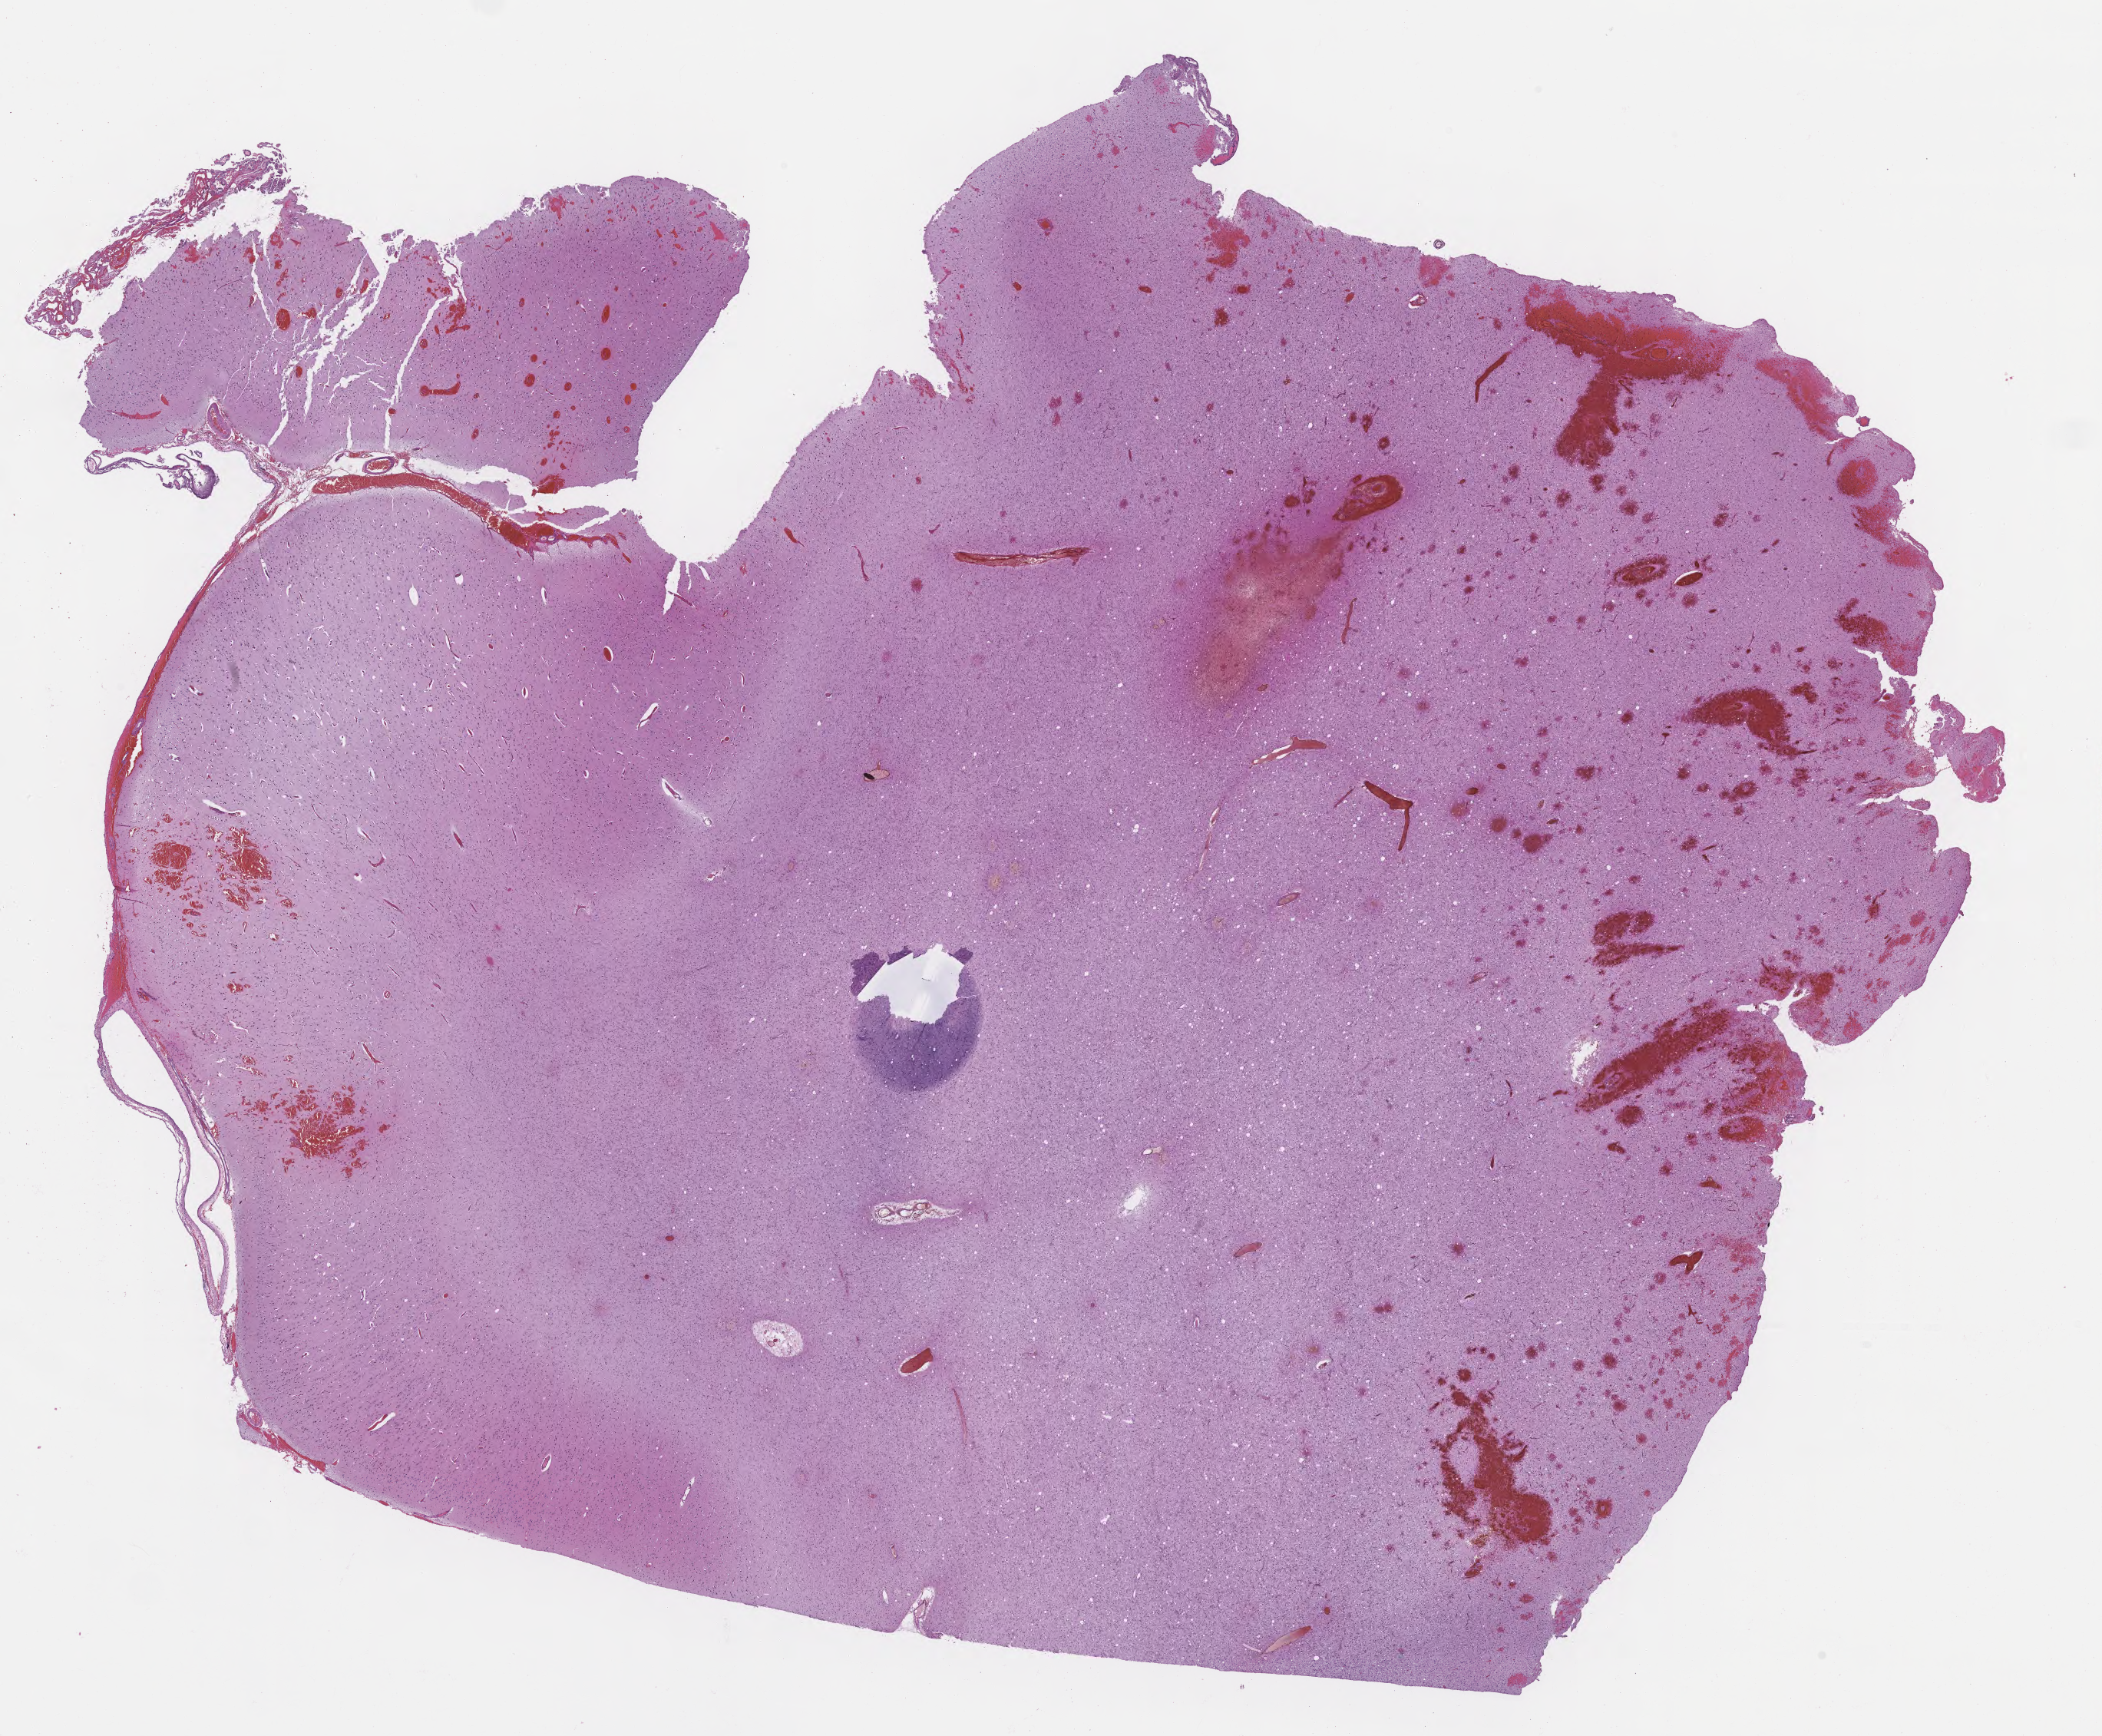
Hematoxylin and eosin (H&E) whole-slide image of tumor tissue from the temporal lobe, shown as a low-resolution overview of the whole scanned area (about 22.1 x 18.3 mm), formalin-fixed, paraffin-embedded (FFPE) tissue. Male patient, age 161 months (13 years 5 months).
Recorded diagnosis: Astrocytoma, NOS.